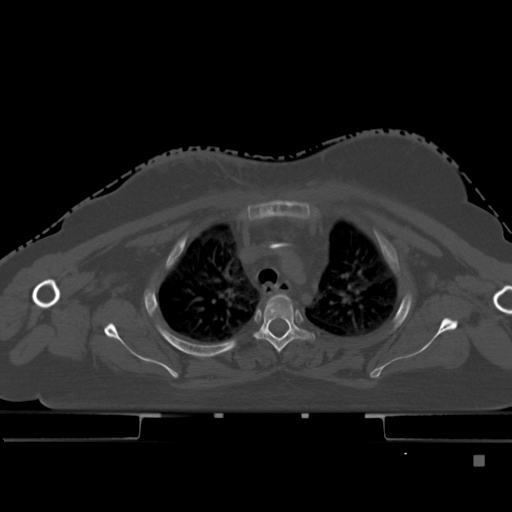
CT including the spine, one axial slice. Slice 347 of 495 in the series (ordered by position). Bone window (W 1800 / L 400 HU). 1.5 mm slice thickness. 512 × 512 image matrix, field of view 404 × 404 mm. Female patient, age 33 years. From the clinical record (not read from this slice): primary cancer: breast; vertebrae with lytic lesions (as recorded): T1.
Structures marked on this image (semi-automatic segmentation, software-assisted and operator-edited):
- T2 vertebra: bounding box <270,294,289,301> (left, top, right, bottom; pixels)
- T3 vertebra: <255,301,312,353>